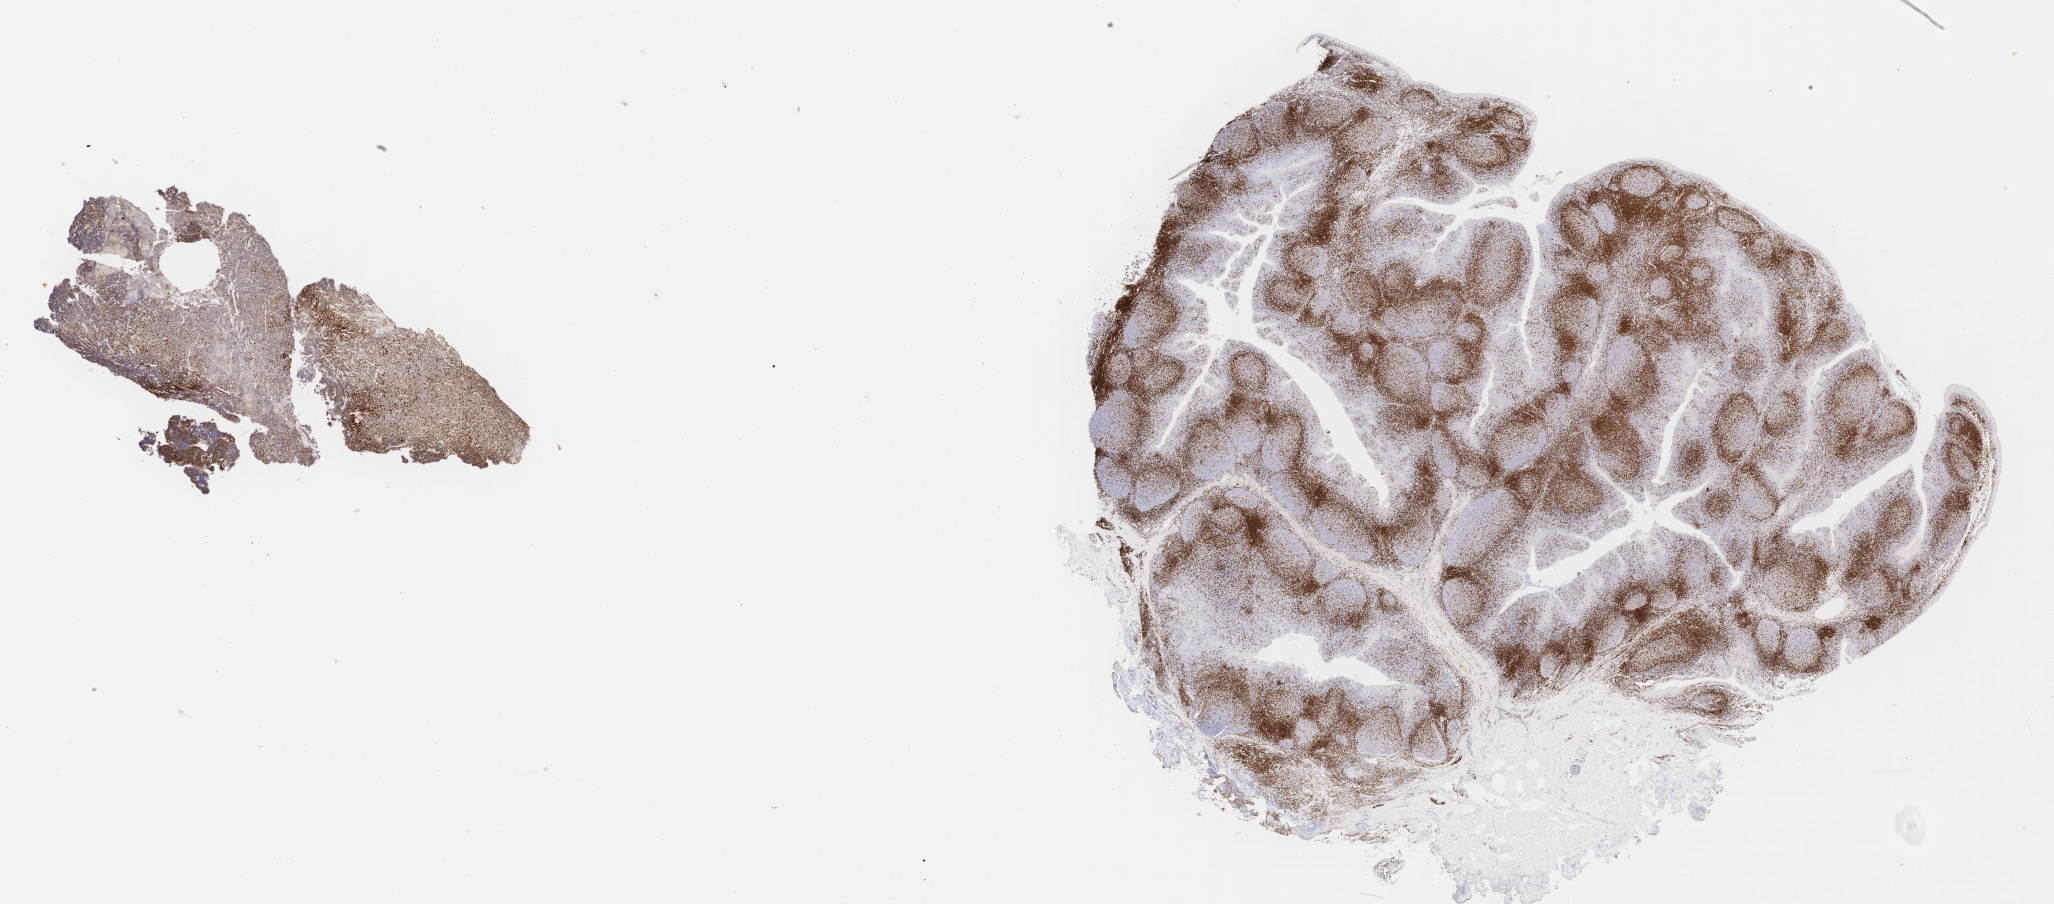
Immunohistochemistry (IHC) whole-slide image stained for CD3, a low-resolution overview of the entire scanned area, about 33.2 x 14.6 mm; tumor tissue; anatomic site: mandible. Male patient, 25 years old.
Diagnosis: Diffuse large B-cell lymphoma, NOS.